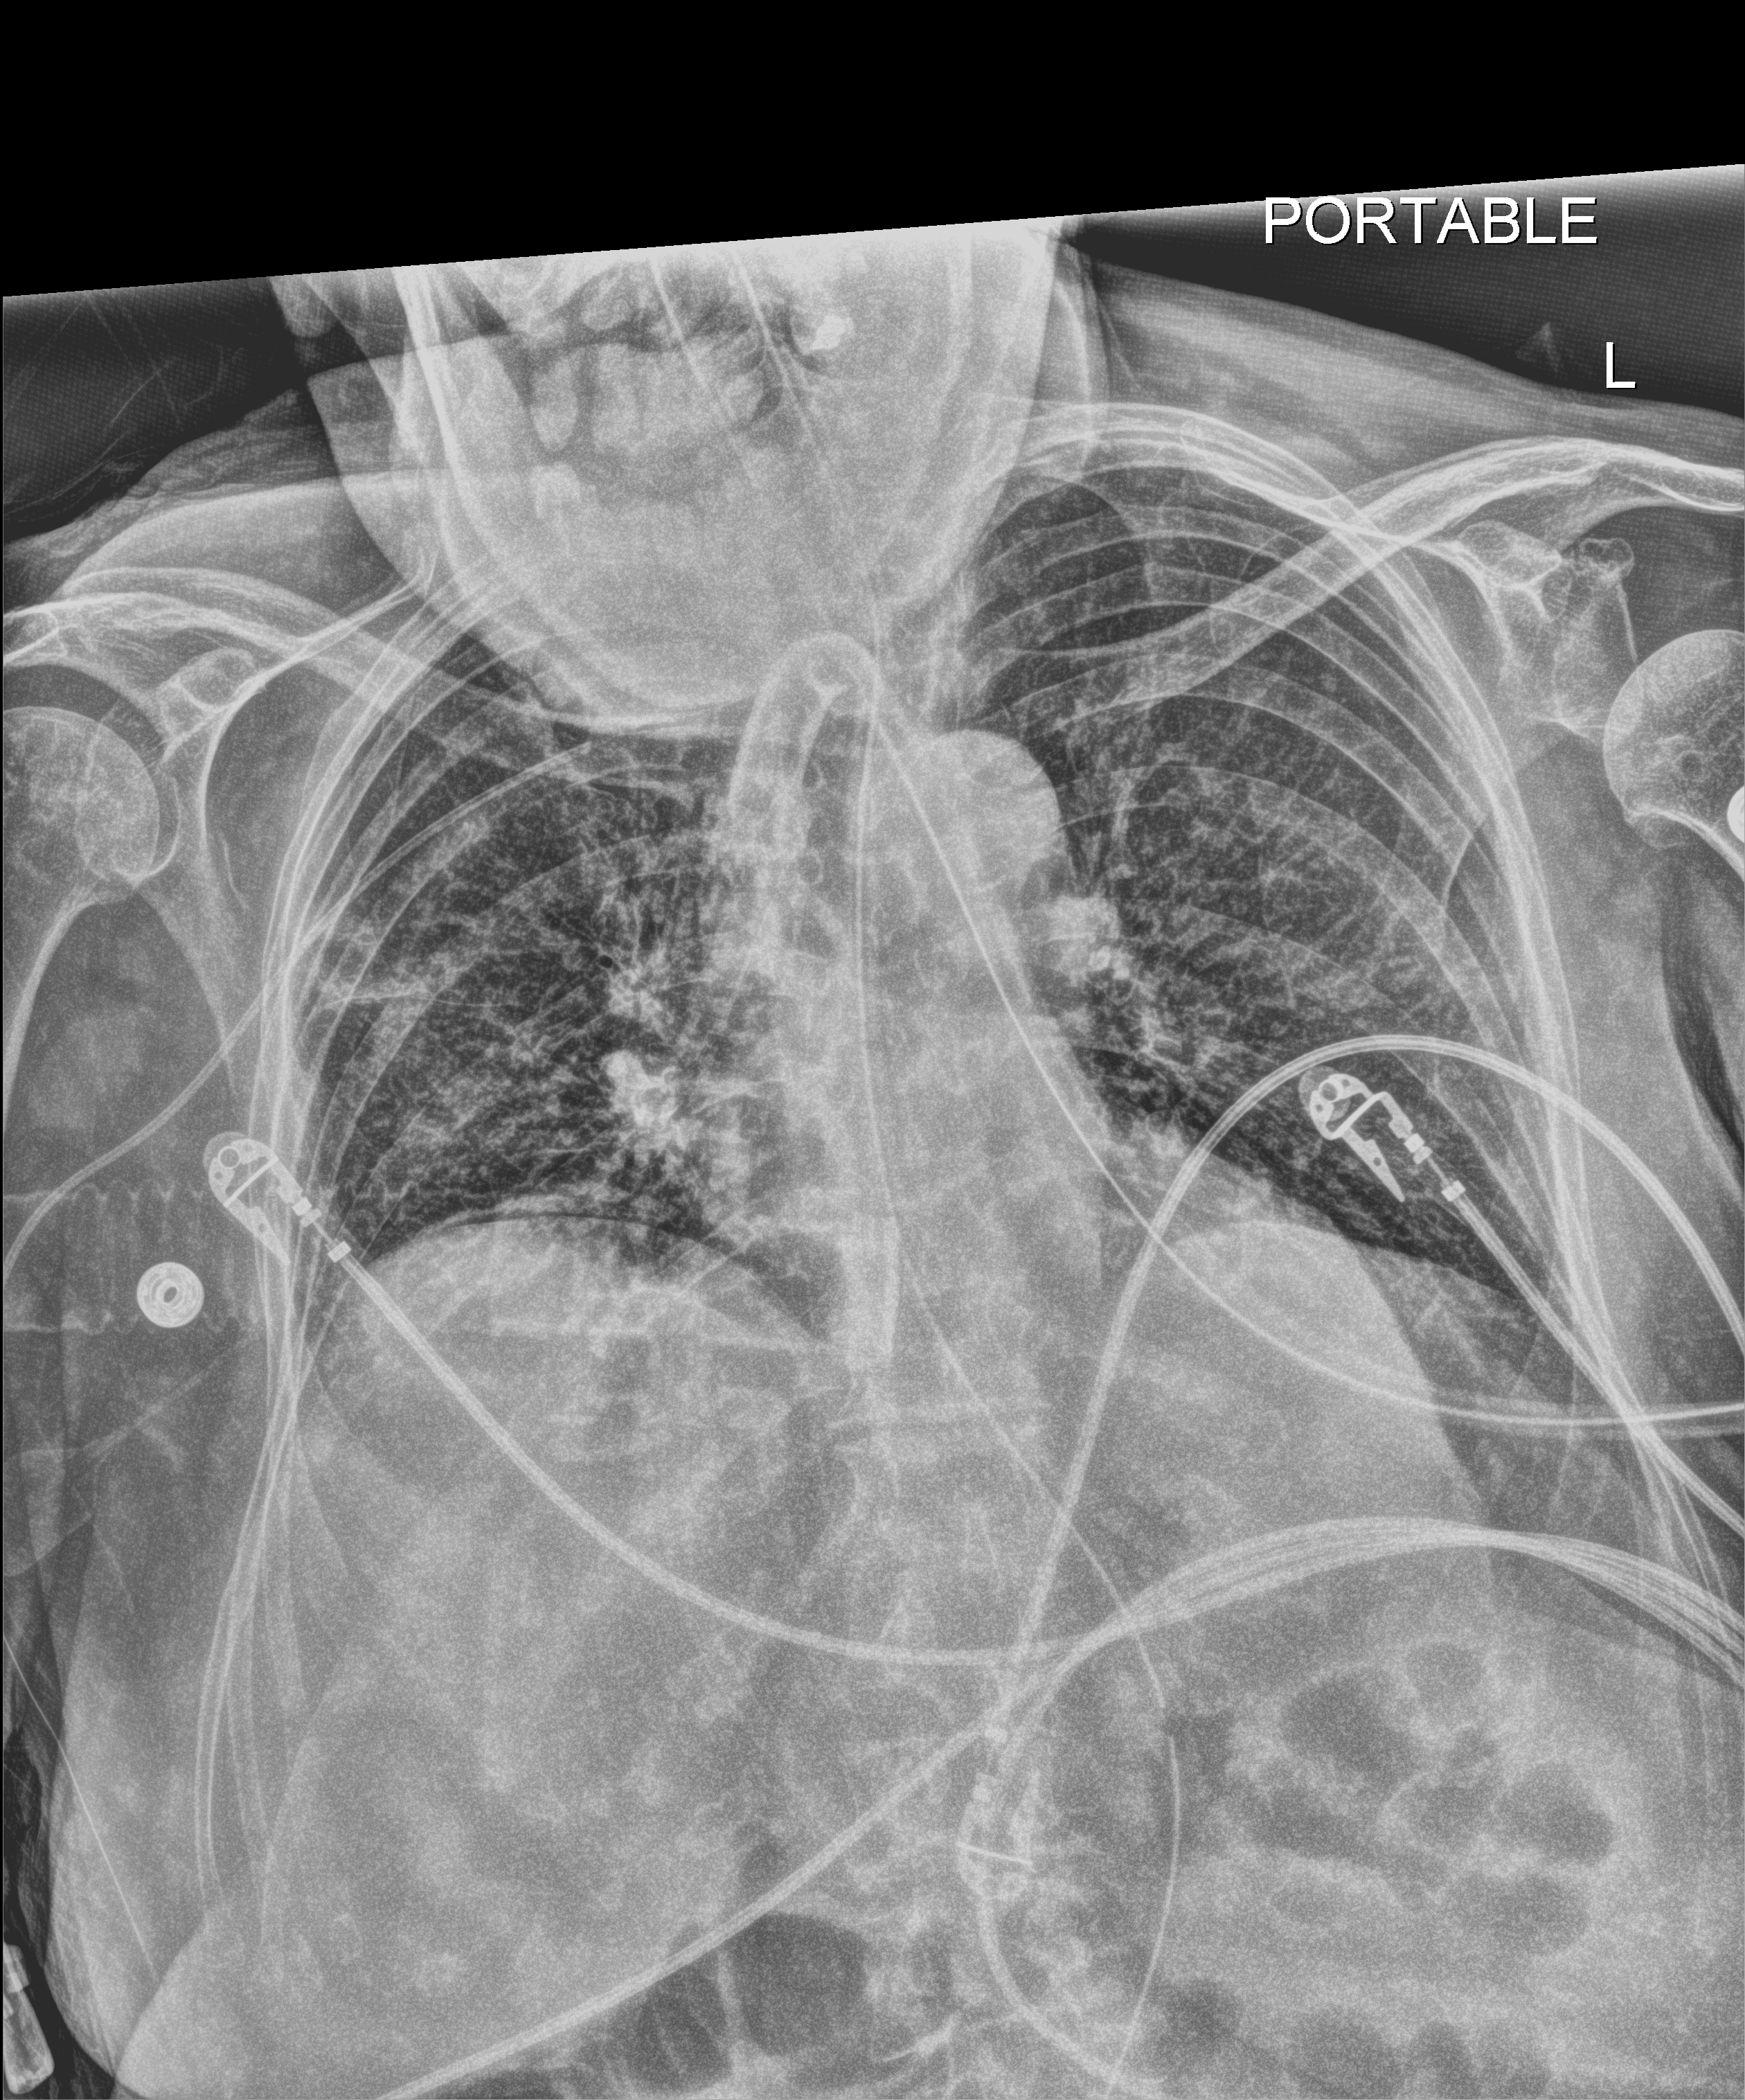
Chest radiograph (digital radiography), anteroposterior (AP) projection. Female patient hospitalised with COVID-19, age 75–90 years.
Hospital-stay facts (about this admission, not read from this image; timing relative to this image not recorded): admitted to intensive care during this hospital stay: yes; length of hospital stay: 82 days.